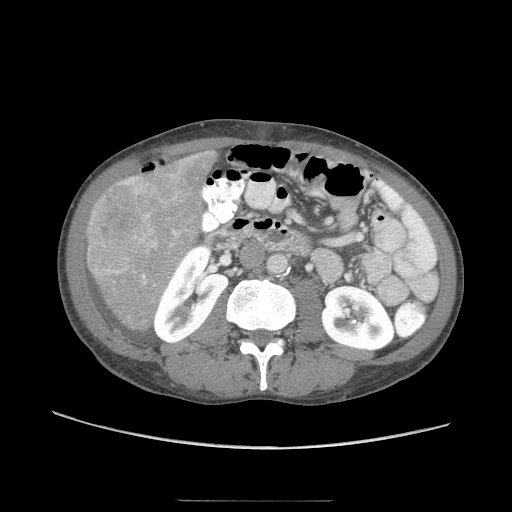
Contrast-enhanced abdominal CT (liver protocol), one axial slice. Slice 17 of 103 in the series (ordered by position). Soft-tissue window (W 400 / L 40 HU). 2.5 mm slice thickness. 512 × 512 image matrix. Case-level facts recorded for this patient, not image findings: diagnosis: hepatocellular carcinoma (patient treated with transarterial chemoembolisation; whether this scan precedes or follows treatment is not stated here); TNM stage (as recorded): Stage-IIIA; Child-Pugh class: A; tumour differentiation: moderately differentiated; tumour nodularity: multinodular.
Structures marked on this image (semi-automatic segmentation, software-assisted and operator-edited):
- liver parenchyma outside the tumour (the mass and vessels are separate outlines, so this box may not span the whole liver): bounding box (x1, y1, x2, y2) in pixels: (86, 150, 218, 330)
- mass: (86, 173, 160, 278)